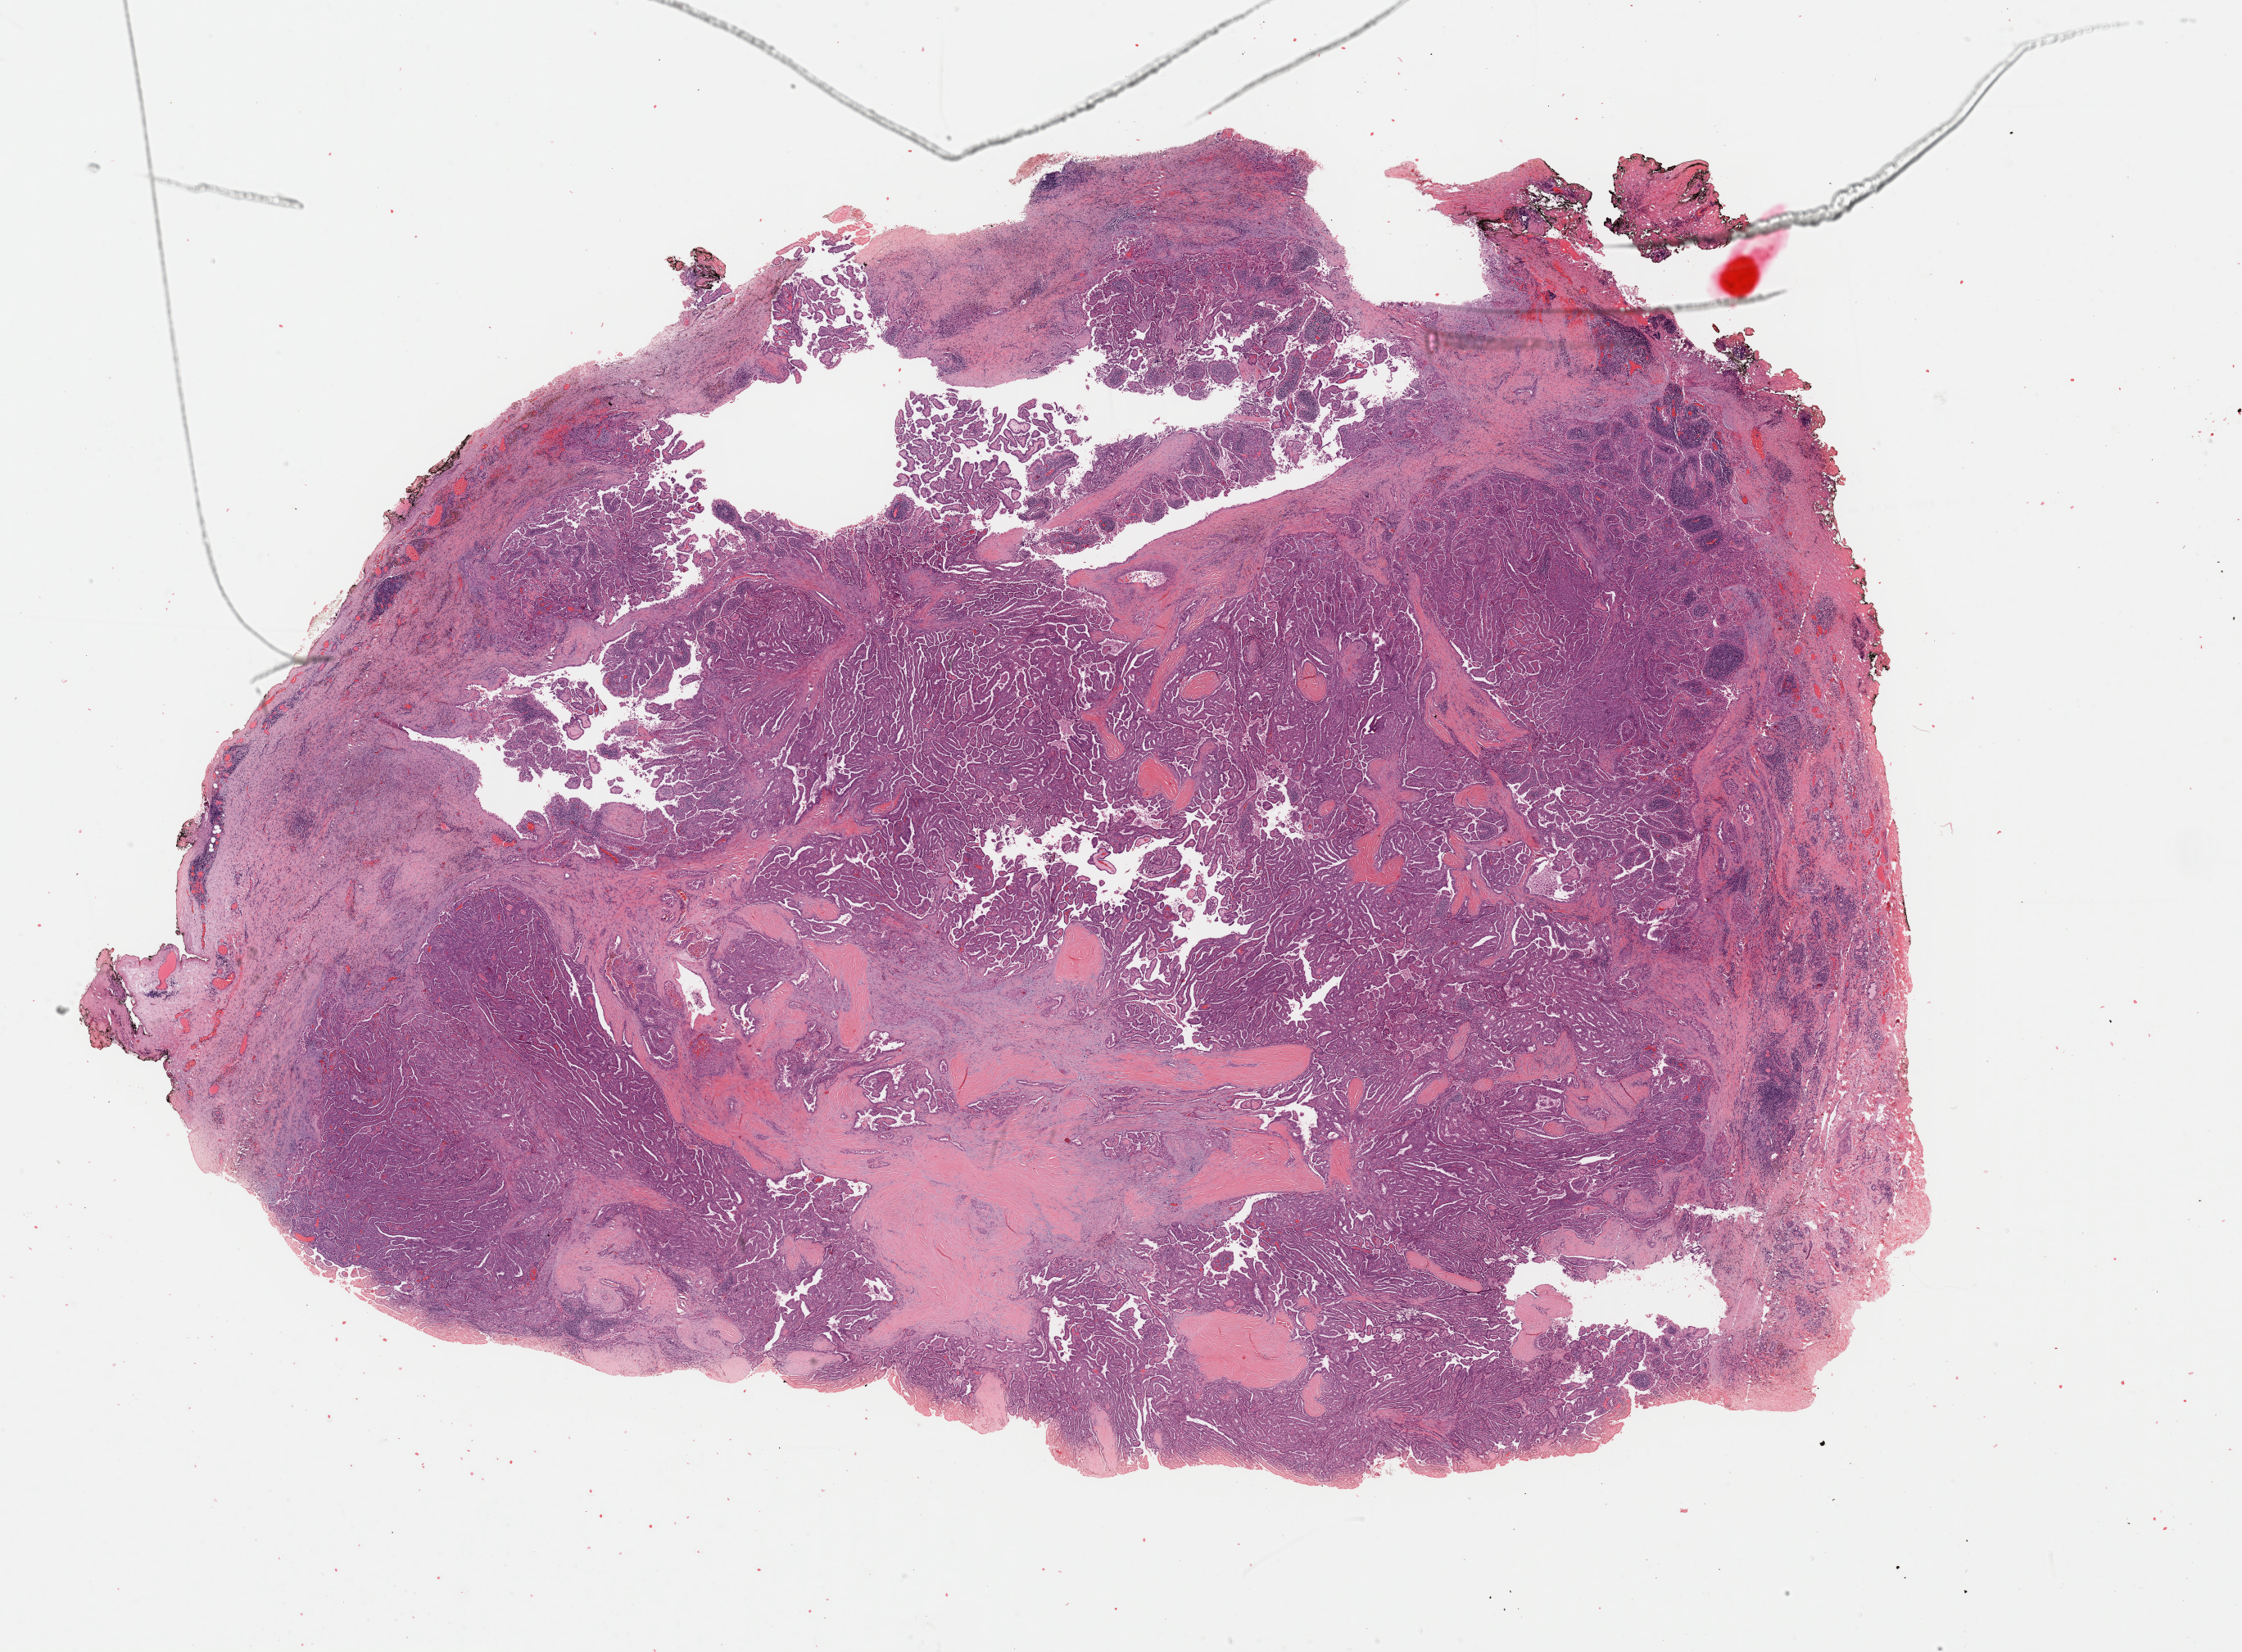
H&E whole-slide image, low-resolution overview of the scanned area, about 21.6 x 15.9 mm (slide scanned at 40x), formalin-fixed paraffin-embedded (FFPE) diagnostic section, sample: primary tumour, thyroid. Female patient; age at initial diagnosis 38 years.
* laterality: midline
* histologic diagnosis: Papillary adenocarcinoma, NOS (thyroid gland)
* lymph nodes positive (case pathology): 0 of 1 examined
* AJCC pathologic stage: I (5th edition)